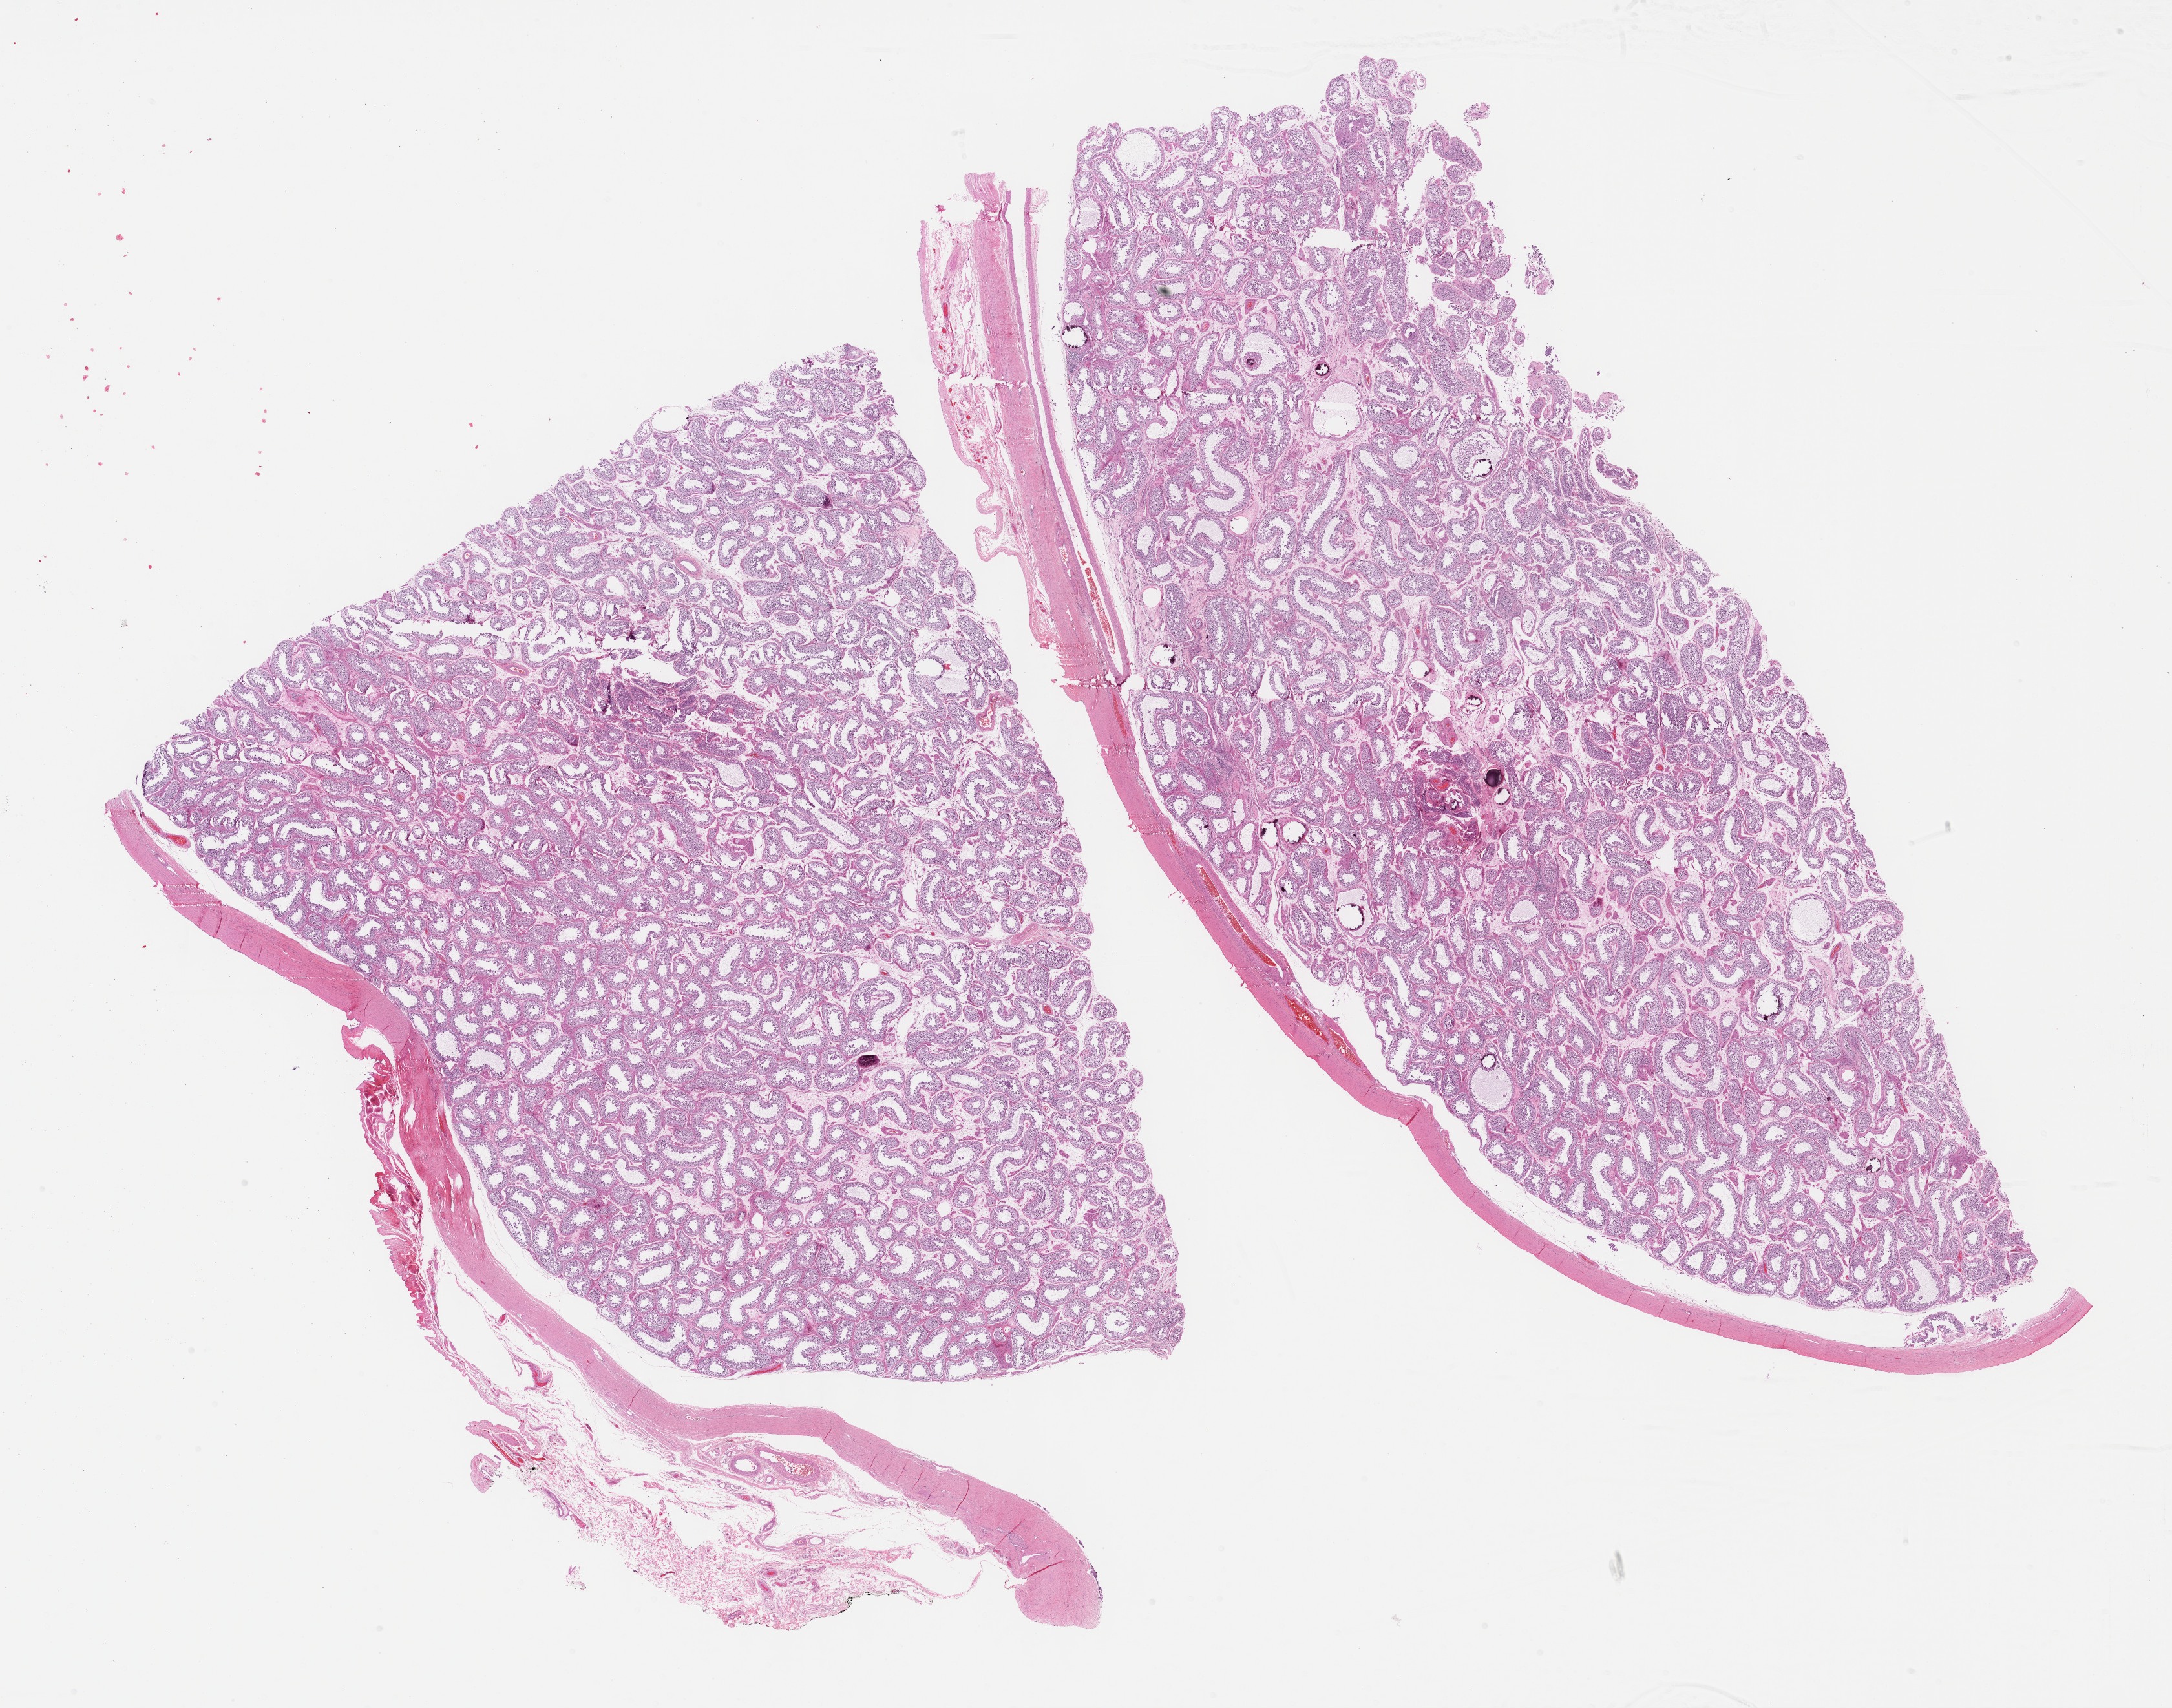
Whole-slide histology image, H&E — whole scanned area (about 27.2 x 21.4 mm, slide scanned at 40x) shown as a low-resolution overview, FFPE section, testis, primary tumour sample. Patient: male, age at initial diagnosis 38 years.
* laterality: left
* diagnosis: Seminoma, NOS